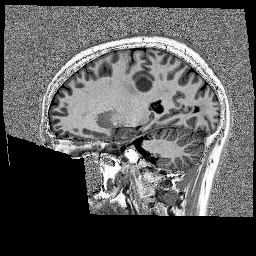
Brain MRI from a brain-tumour surgery series, one sagittal slice. Slice 70 of 176 in the series (ordered by position). 256 × 256 image matrix, field of view 256 × 256 mm. Case-level facts recorded for this patient, not image findings: histopathology: Glioblastoma; WHO grade: 4; IDH mutation: no; tumour location: Left Frontal.
Structures marked on this image (manually delineated by an expert):
- tumour: bounding box (x1, y1, x2, y2) in pixels: (138, 65, 160, 88)